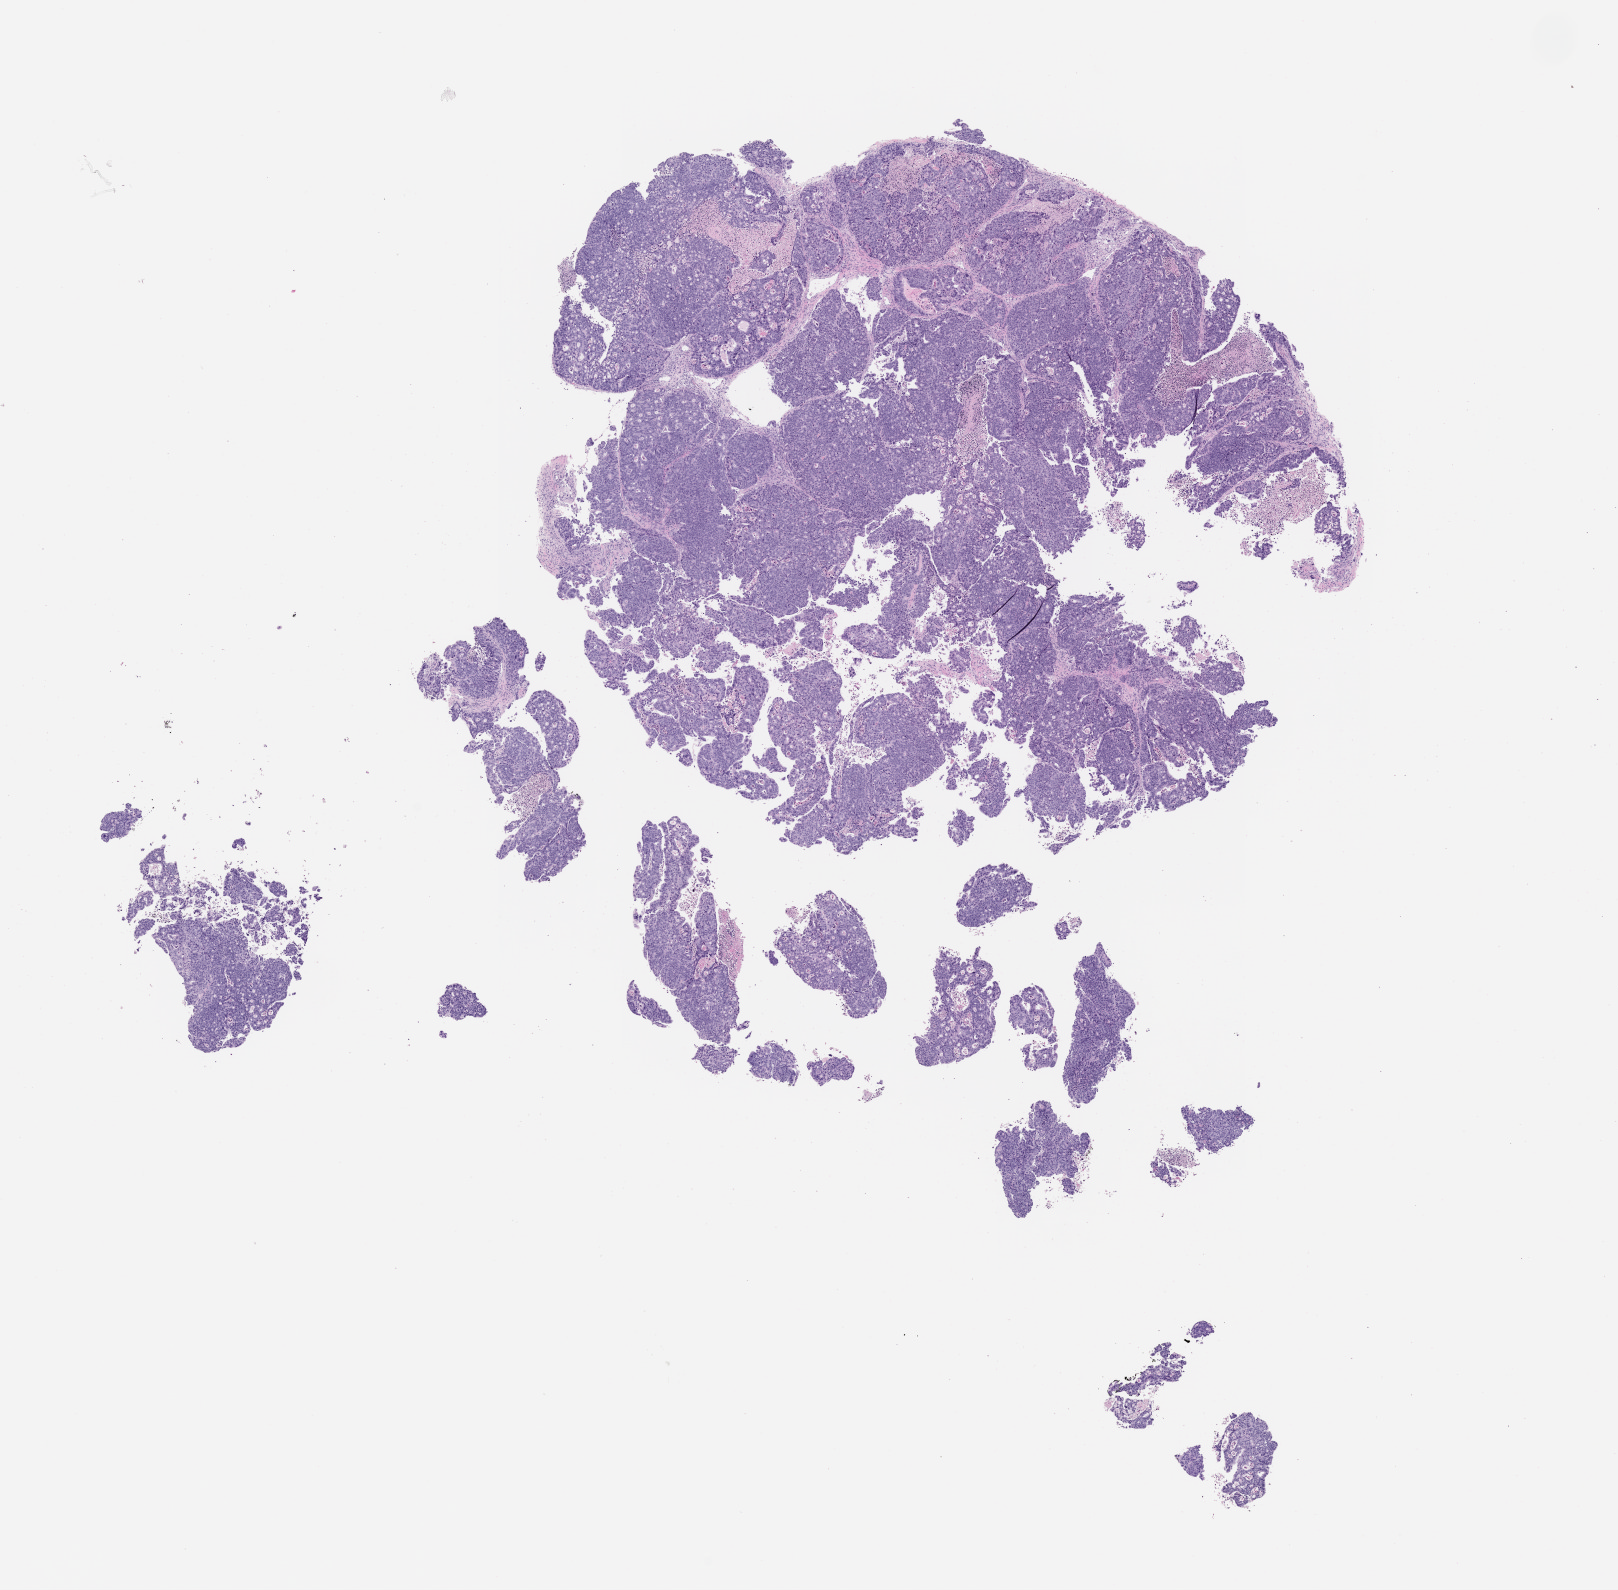
Hematoxylin and eosin (H&E) whole-slide image of a patient-derived xenograft (PDX) tumor grown in a mouse, passage 1, shown as a low-resolution overview of the whole scanned area (about 13.0 x 12.8 mm); formalin-fixed, paraffin-embedded (FFPE) tissue; originating tumor site category: colon.
Originating patient diagnosis: Colon Adenocarcinoma.